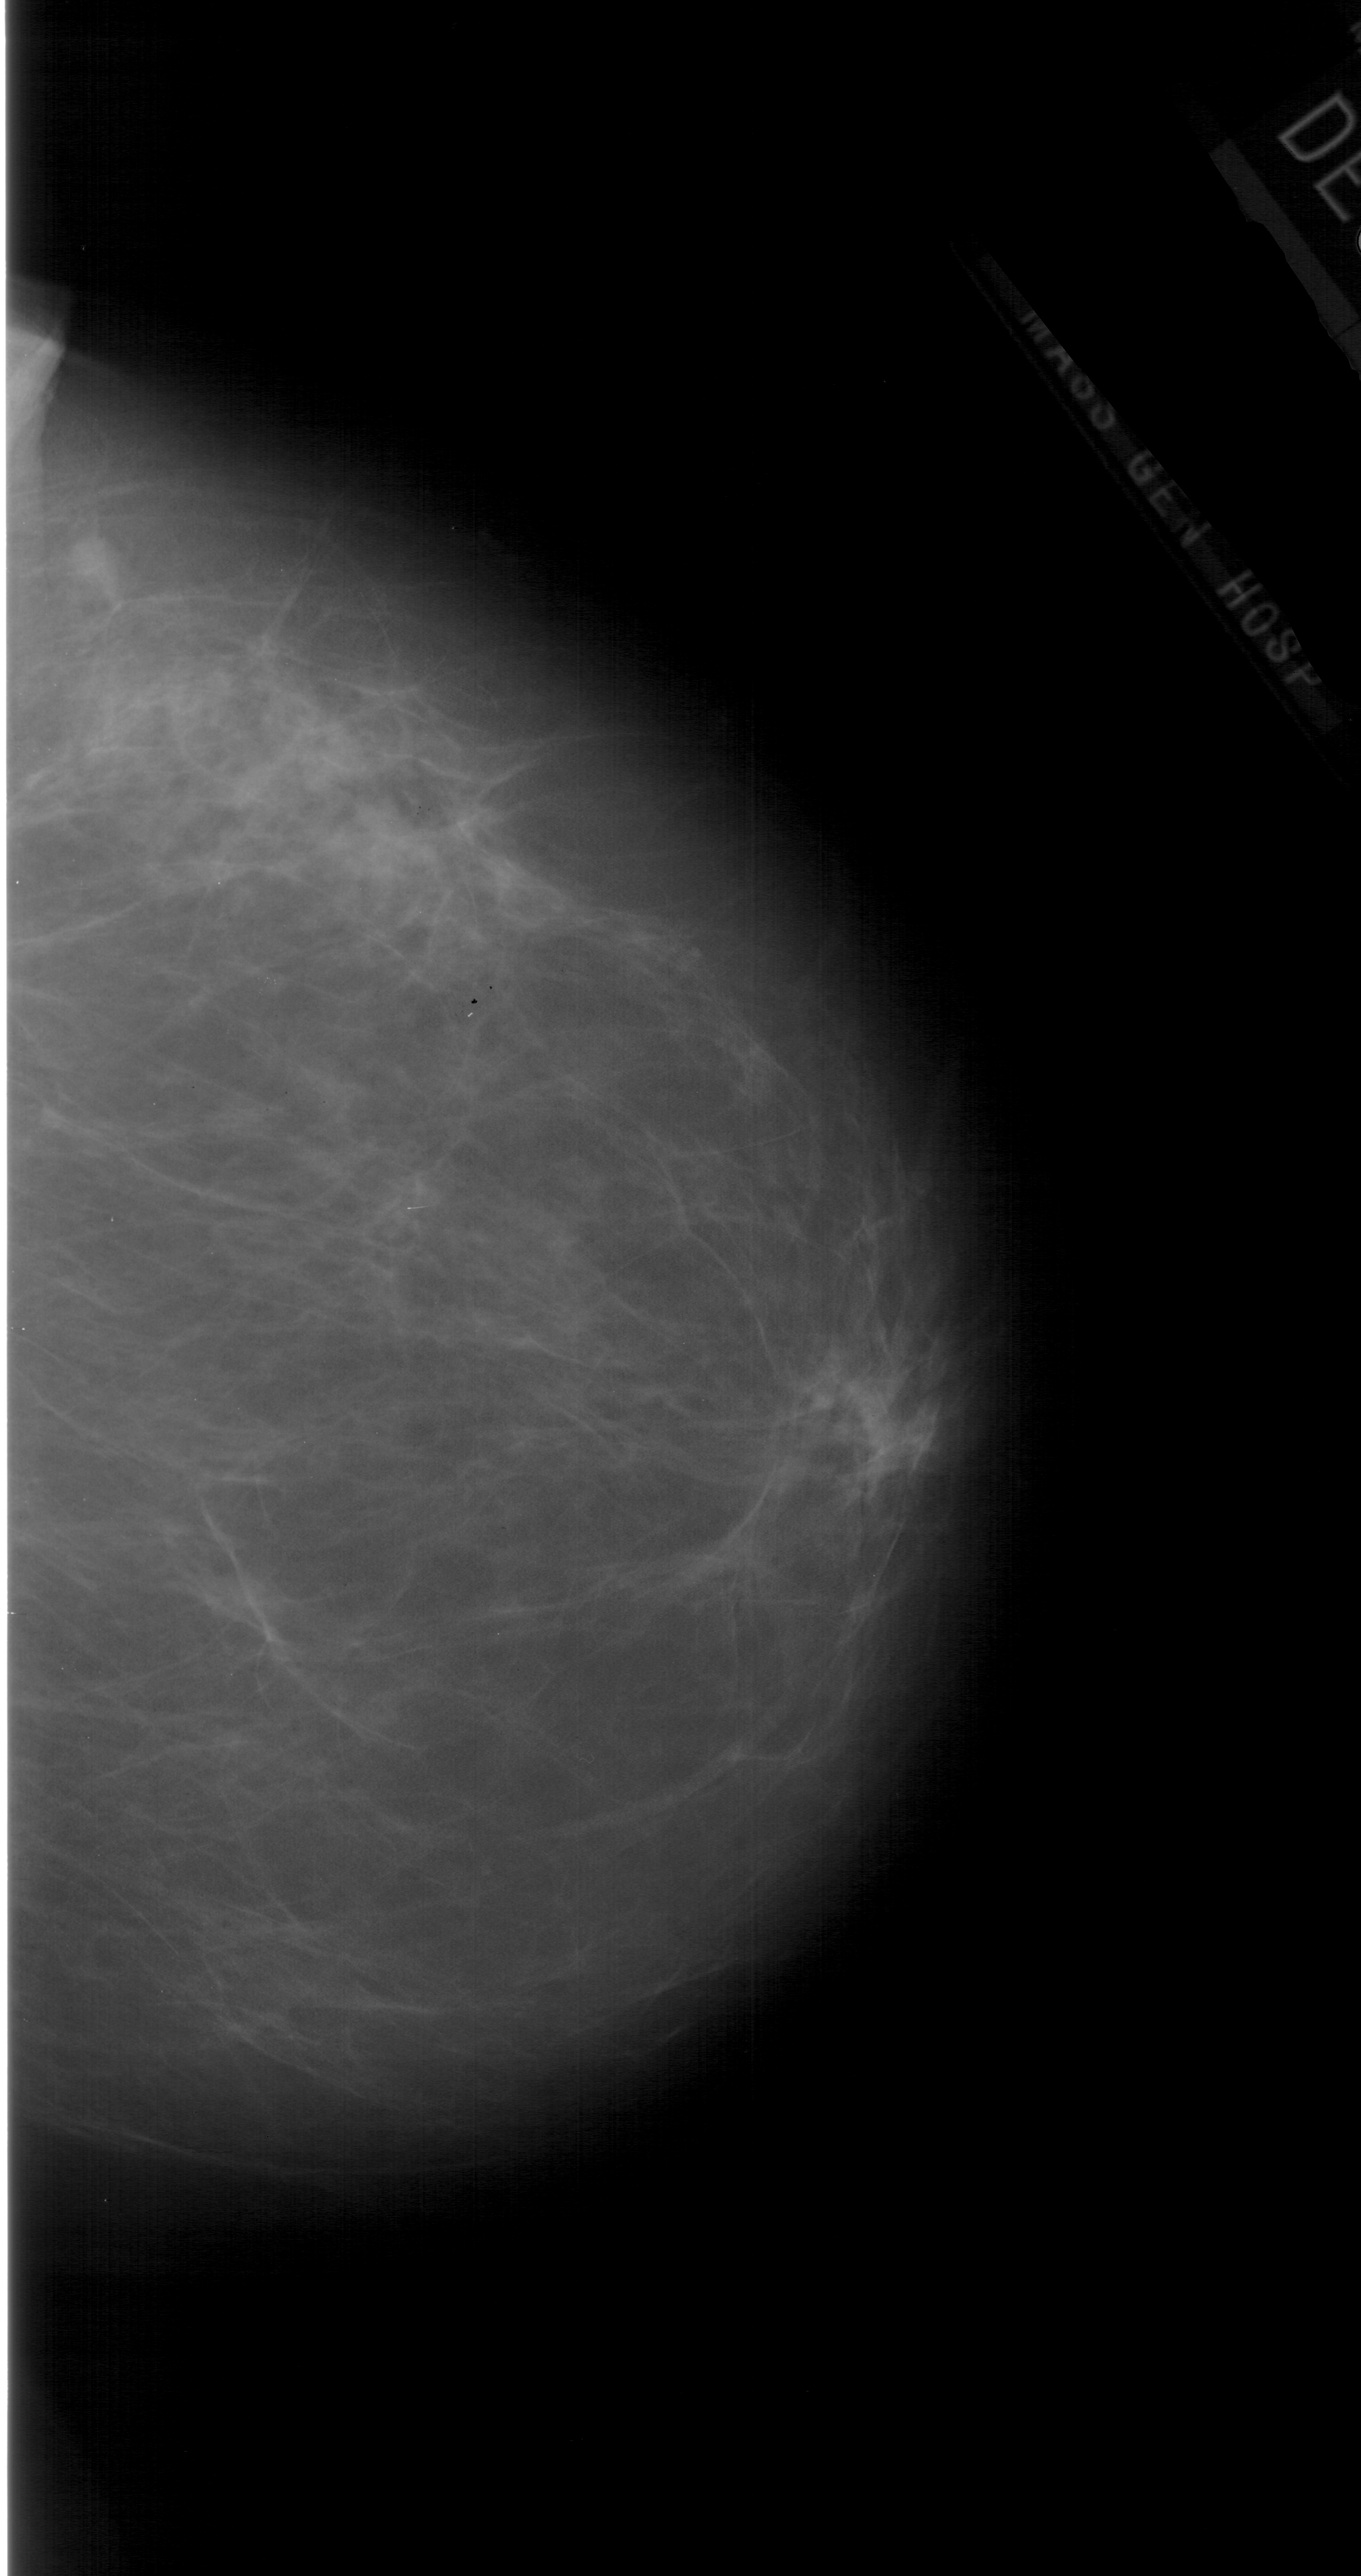
Scanned film-screen mammogram, right breast, craniocaudal (CC) view.
Mass, shape irregular, margins ill defined; BI-RADS assessment category 4; pathology result (as recorded, not read from the image): malignant.